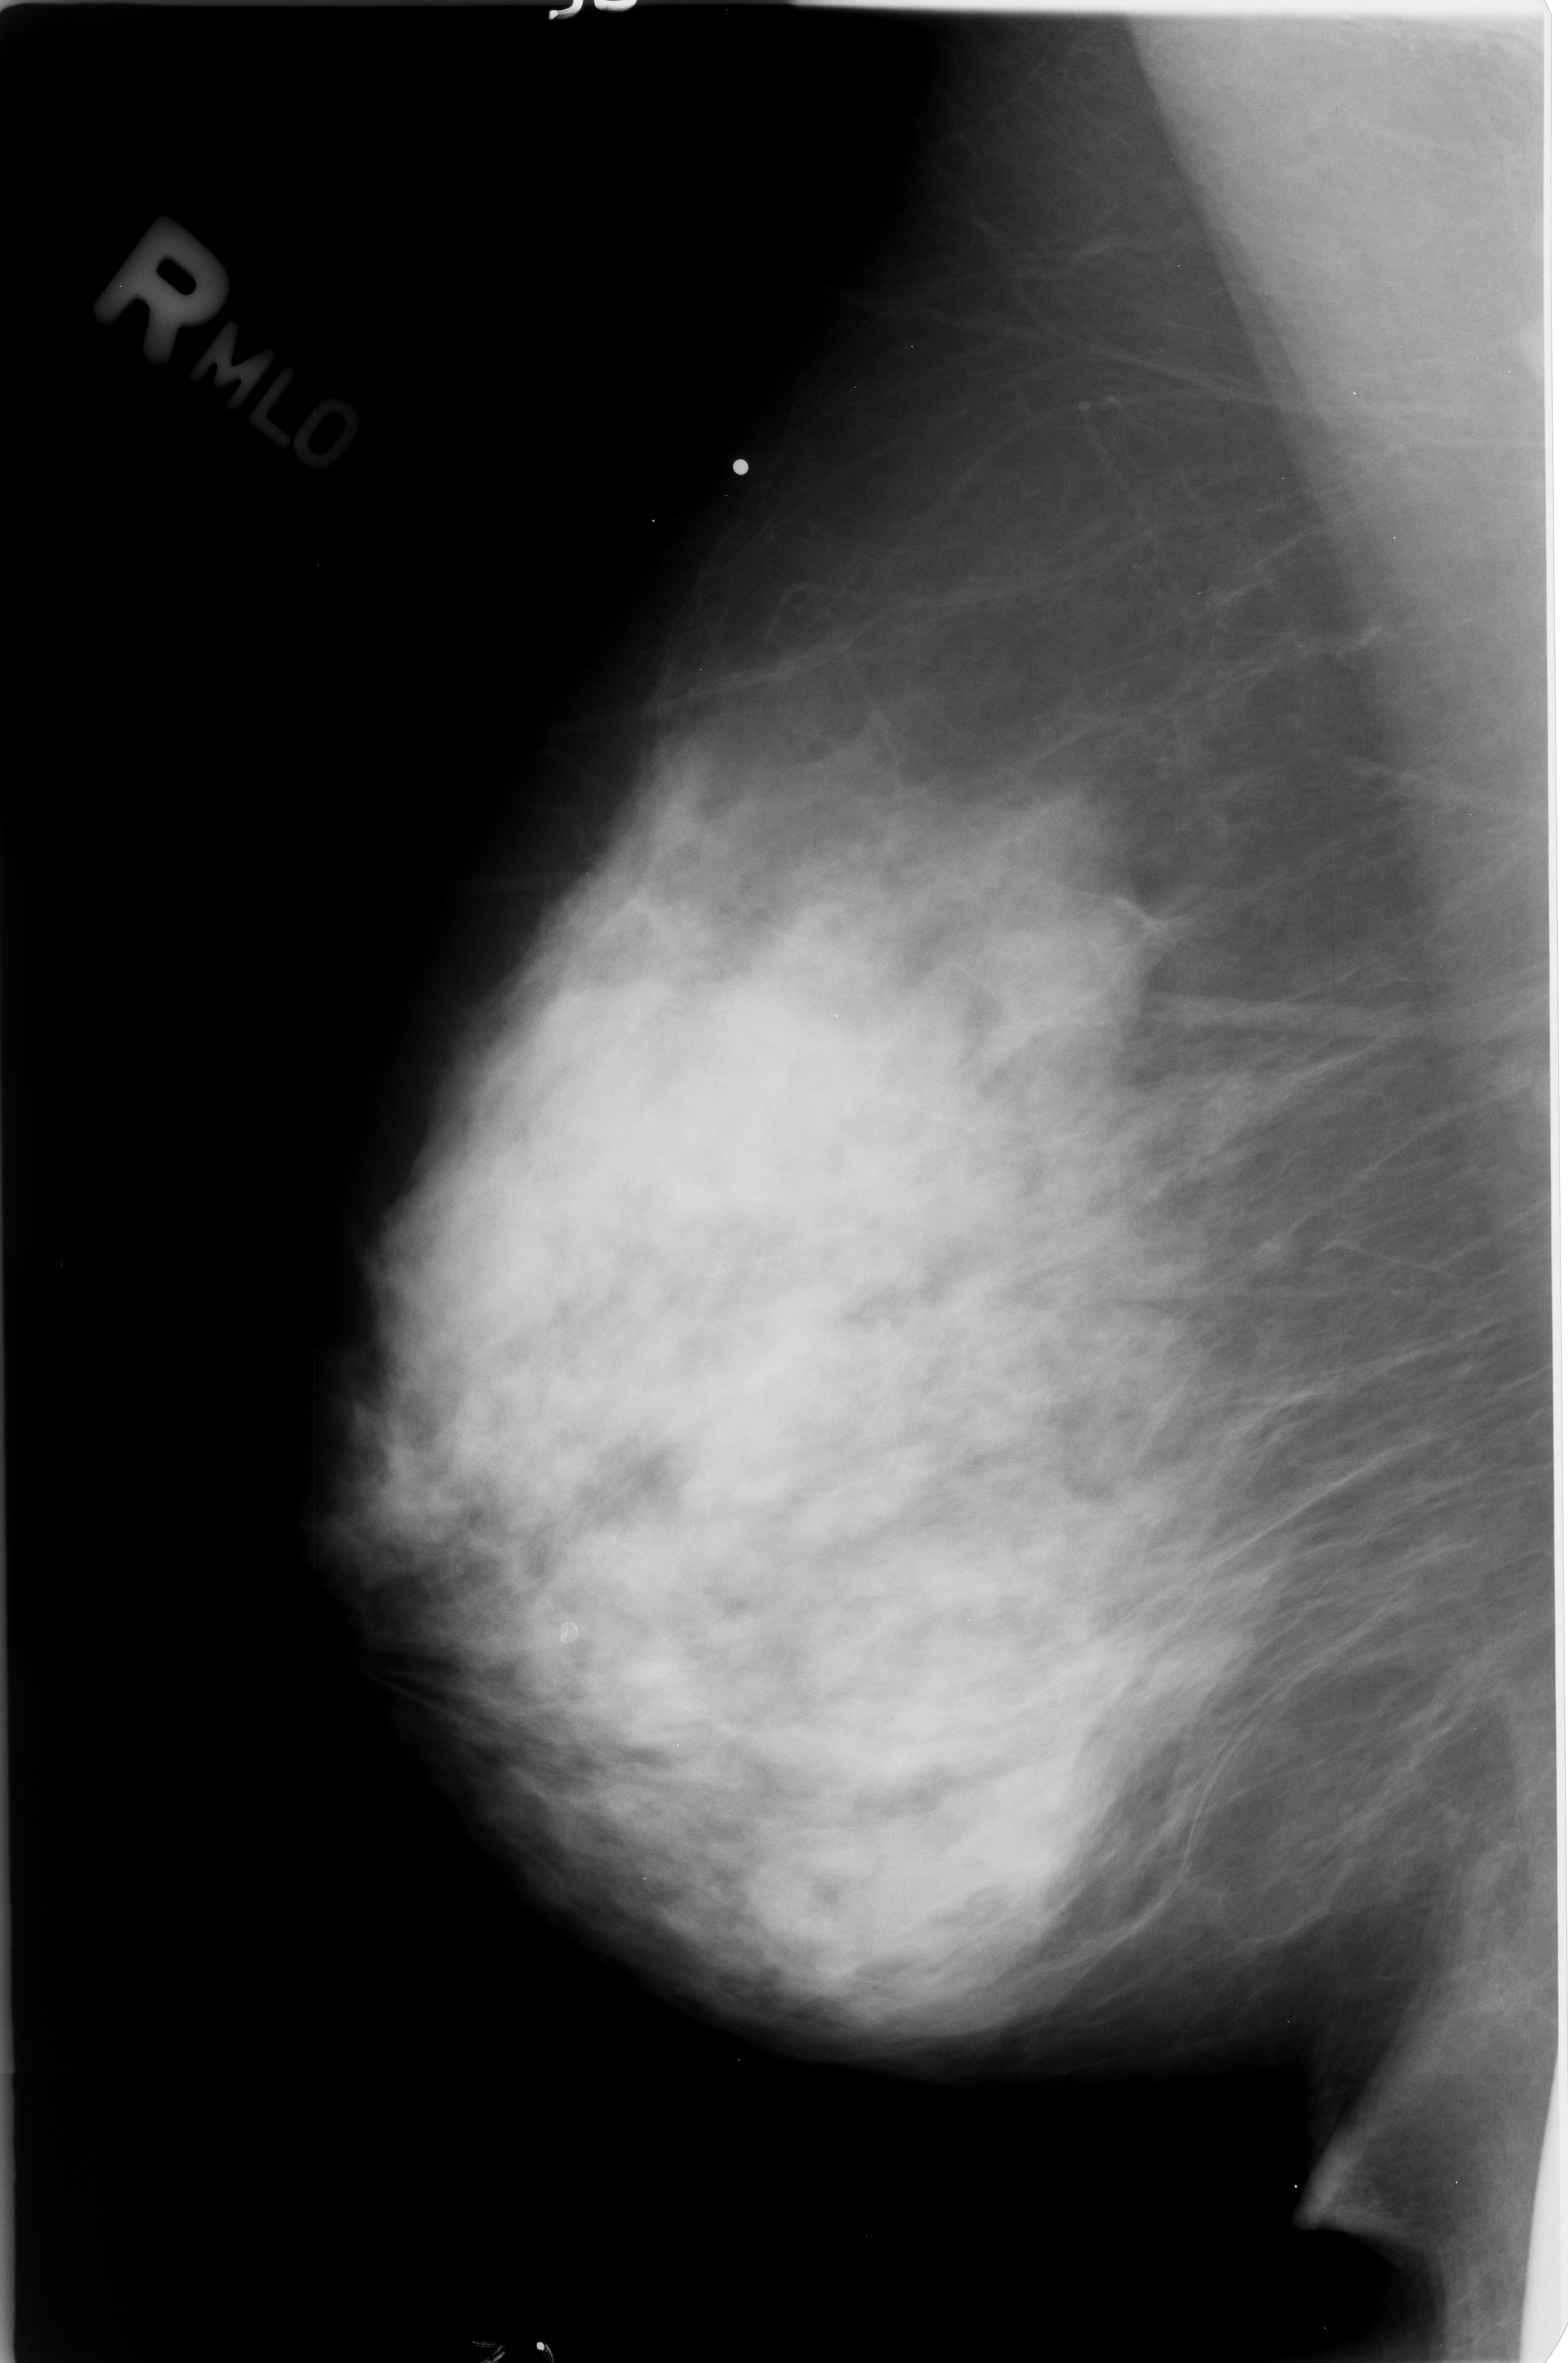
Scanned film-screen mammogram; right breast; MLO view; 1568 × 2363 image matrix.
Marked abnormalities (boxes around the expert regions of interest):
- calcifications, morphology lucent center; BI-RADS assessment category 2; outcome (as recorded, no biopsy): benign without callback (not worked up further): box from (x=554, y=1609) to (x=588, y=1652) px